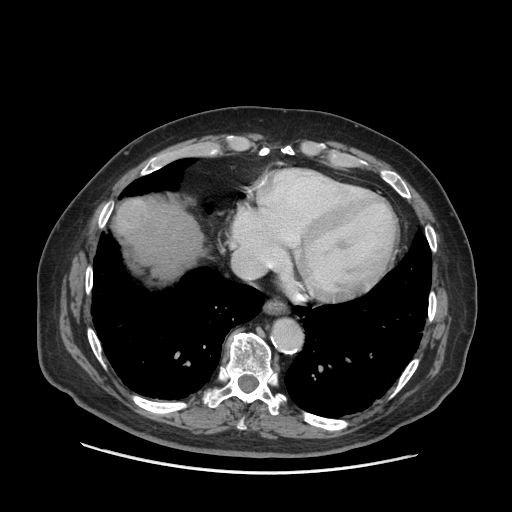
Contrast-enhanced abdominal CT (liver protocol), one axial slice. Slice 65 of 77 in the series (ordered by position). 140 kVp. Soft-tissue window (W 400 / L 40 HU). 2.5 mm slice thickness. 512 × 512 image matrix, field of view 420 × 420 mm. From the clinical record (not read from this slice): diagnosis: hepatocellular carcinoma (patient treated with transarterial chemoembolisation; whether this scan precedes or follows treatment is not stated here); TNM stage (as recorded): Stage-I; Child-Pugh class: A; tumour differentiation: well differentiated.
Outlined on this slice (semi-automatic segmentation, software-assisted and operator-edited):
- abdominal aorta: bounding box <273,322,301,351> (left, top, right, bottom; pixels)
- liver parenchyma outside the tumour (the mass and vessels are separate outlines, so this box may not span the whole liver): <114,198,202,280>
- mass: <115,201,147,232>